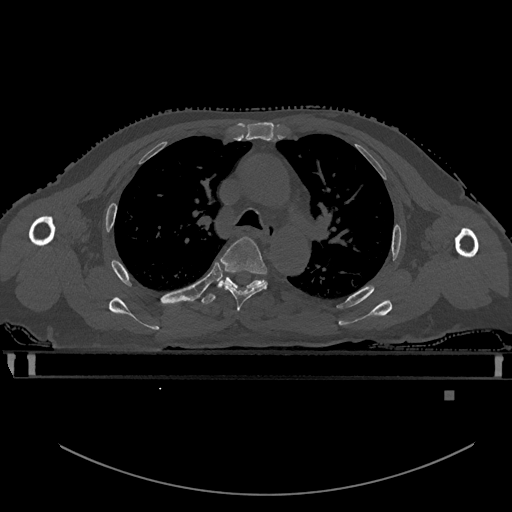
CT including the spine, one axial slice. Position 390 of 969 along the scan axis. Bone window (W 1800 / L 400 HU). 512 × 512 image matrix, field of view 456 × 456 mm. Patient: male, 82 years. Case-level facts recorded for this patient, not image findings: primary cancer: prostate.
Structures marked on this image (semi-automatically segmented with operator editing):
- T4 vertebra: bounding box <220,236,268,312> (left, top, right, bottom; pixels)
- T5 vertebra: <201,272,264,305>